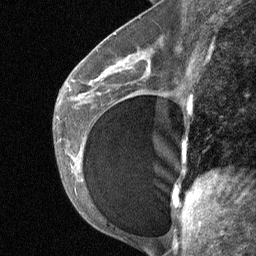
Breast MRI (dynamic contrast-enhanced), one sagittal slice; slice 37 of 64 in the series (ordered by position); dynamic contrast-enhanced study with each time point stored as its own series, time point 2 of 3 at this slice position (early post-contrast, ordered by acquisition time); 1.5 T; TE 4.8 ms, TR 27 ms; 256 × 256 image matrix, field of view 180 × 180 mm. Female patient, age 35 years. Case-level facts recorded for this patient, not image findings: setting: breast cancer imaged before/during neoadjuvant chemotherapy; receptor status: HR-positive, HER2-negative.
Structures marked on this image (semi-automatic segmentation, software-assisted and operator-edited):
- analysis volume of interest (the breast-tissue region the enhancement analysis was run in; not a lesion): bounding box <74,58,163,171> (left, top, right, bottom; pixels)
- tumour enhancement mask (voxels above the 90 % enhancement threshold inside the analysis volume of interest): <104,69,108,73>